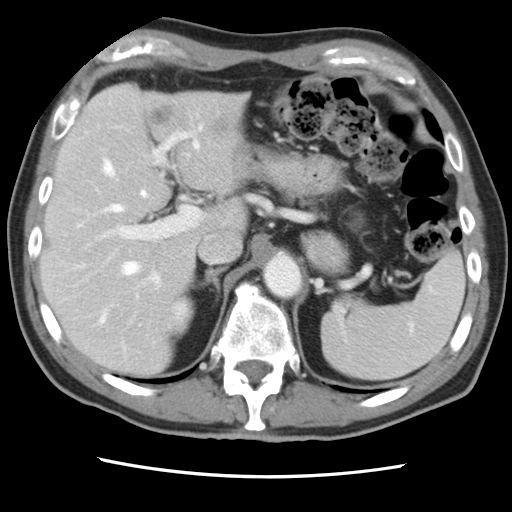
Contrast-enhanced abdominal CT, one axial slice; position 57 of 83 along the scan axis; 120 kVp; intravenous contrast given; soft-tissue window (W 400 / L 40 HU); 5 mm slice thickness; 512 × 512 image matrix, field of view 321 × 321 mm. Male patient, age 69 years. From the clinical record (not read from this slice): diagnosis: colorectal cancer liver metastases, imaged before liver resection; multiple liver metastases: yes; largest metastasis: 3.5 cm; chemotherapy before resection: yes.
Structures marked on this image (outlined manually by an expert reader):
- hepatic veins: bounding box [x1, y1, x2, y2] px = [79, 141, 199, 321]
- liver: [42, 84, 245, 377]
- planned liver remnant (the part of the liver to remain after resection): [42, 141, 205, 377]
- portal vein (with intrahepatic branches): [88, 122, 204, 289]
- liver metastasis: [150, 105, 173, 125]
- liver metastasis: [213, 117, 235, 133]